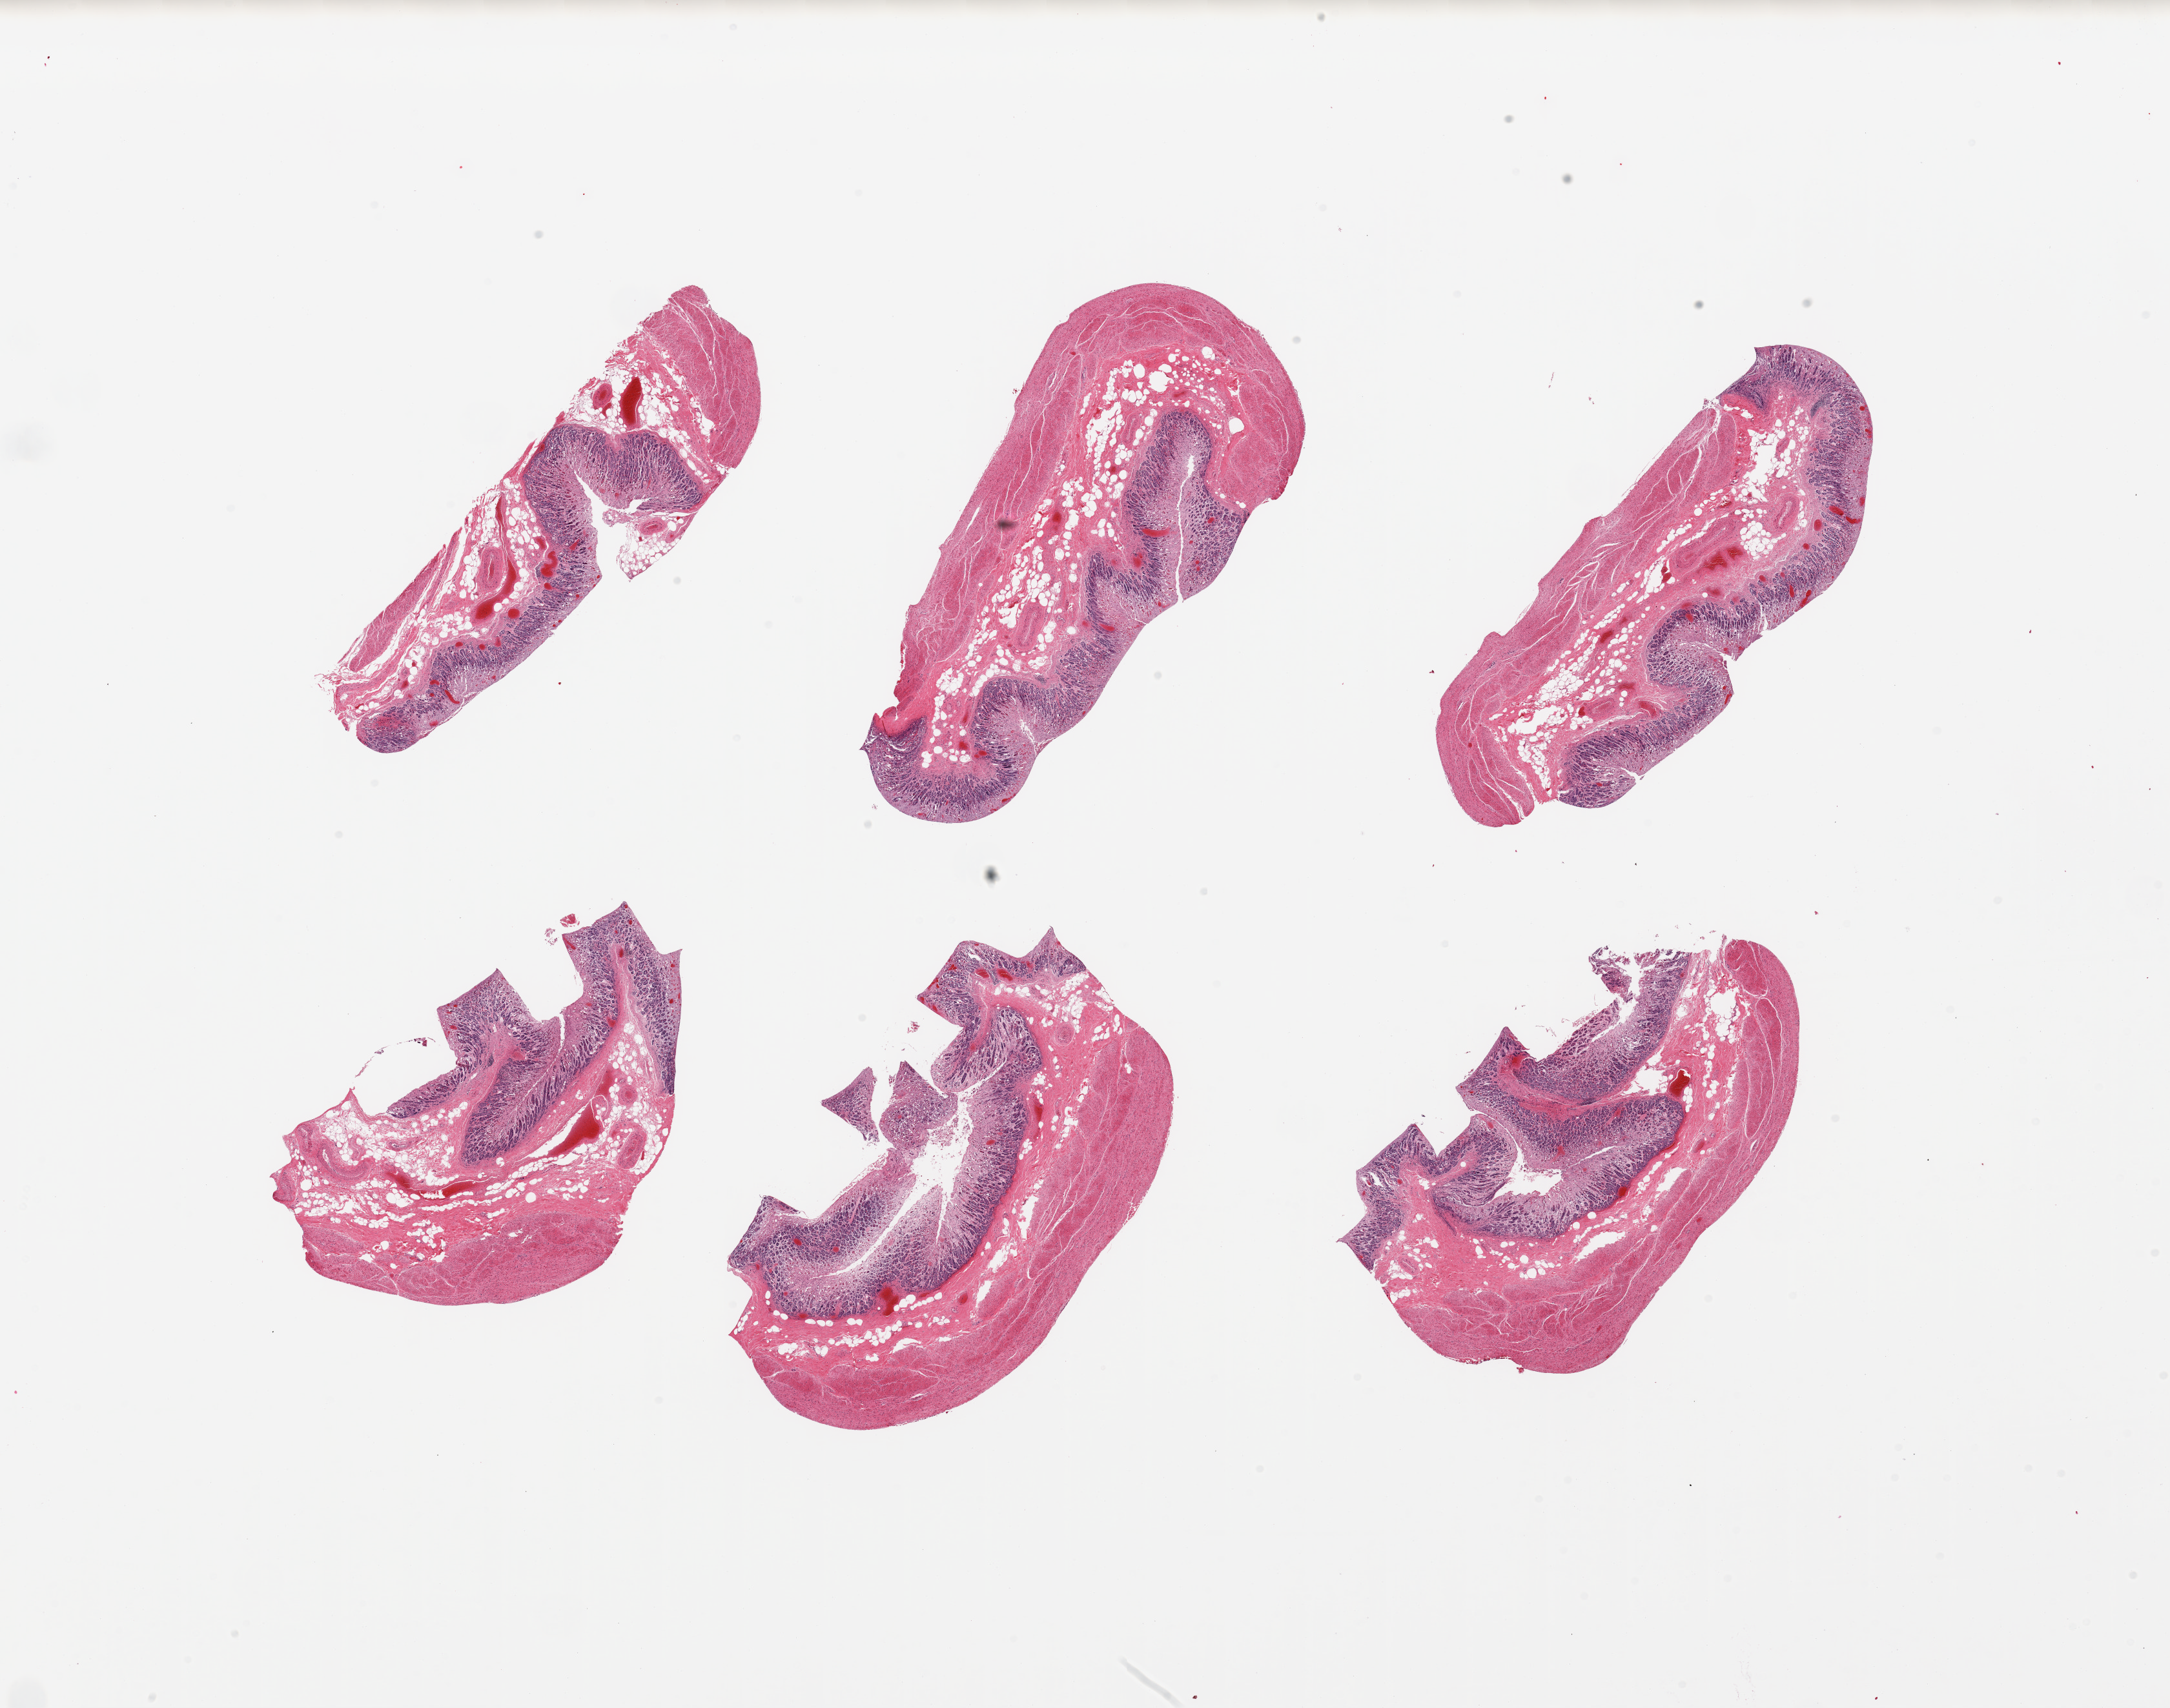
Hematoxylin and eosin (H&E) whole-slide image — shown as a low-resolution overview of the whole scanned area (about 26.6 x 20.9 mm, from a 20x scan). PAXgene-fixed, paraffin-embedded tissue. Section of stomach (target tissue). Tissue donor sample.
- pathologist's review note for this sample: 6 pieces, mucosa up to ~0.5mm, ~20% thickness, moderate-advanced autolysis